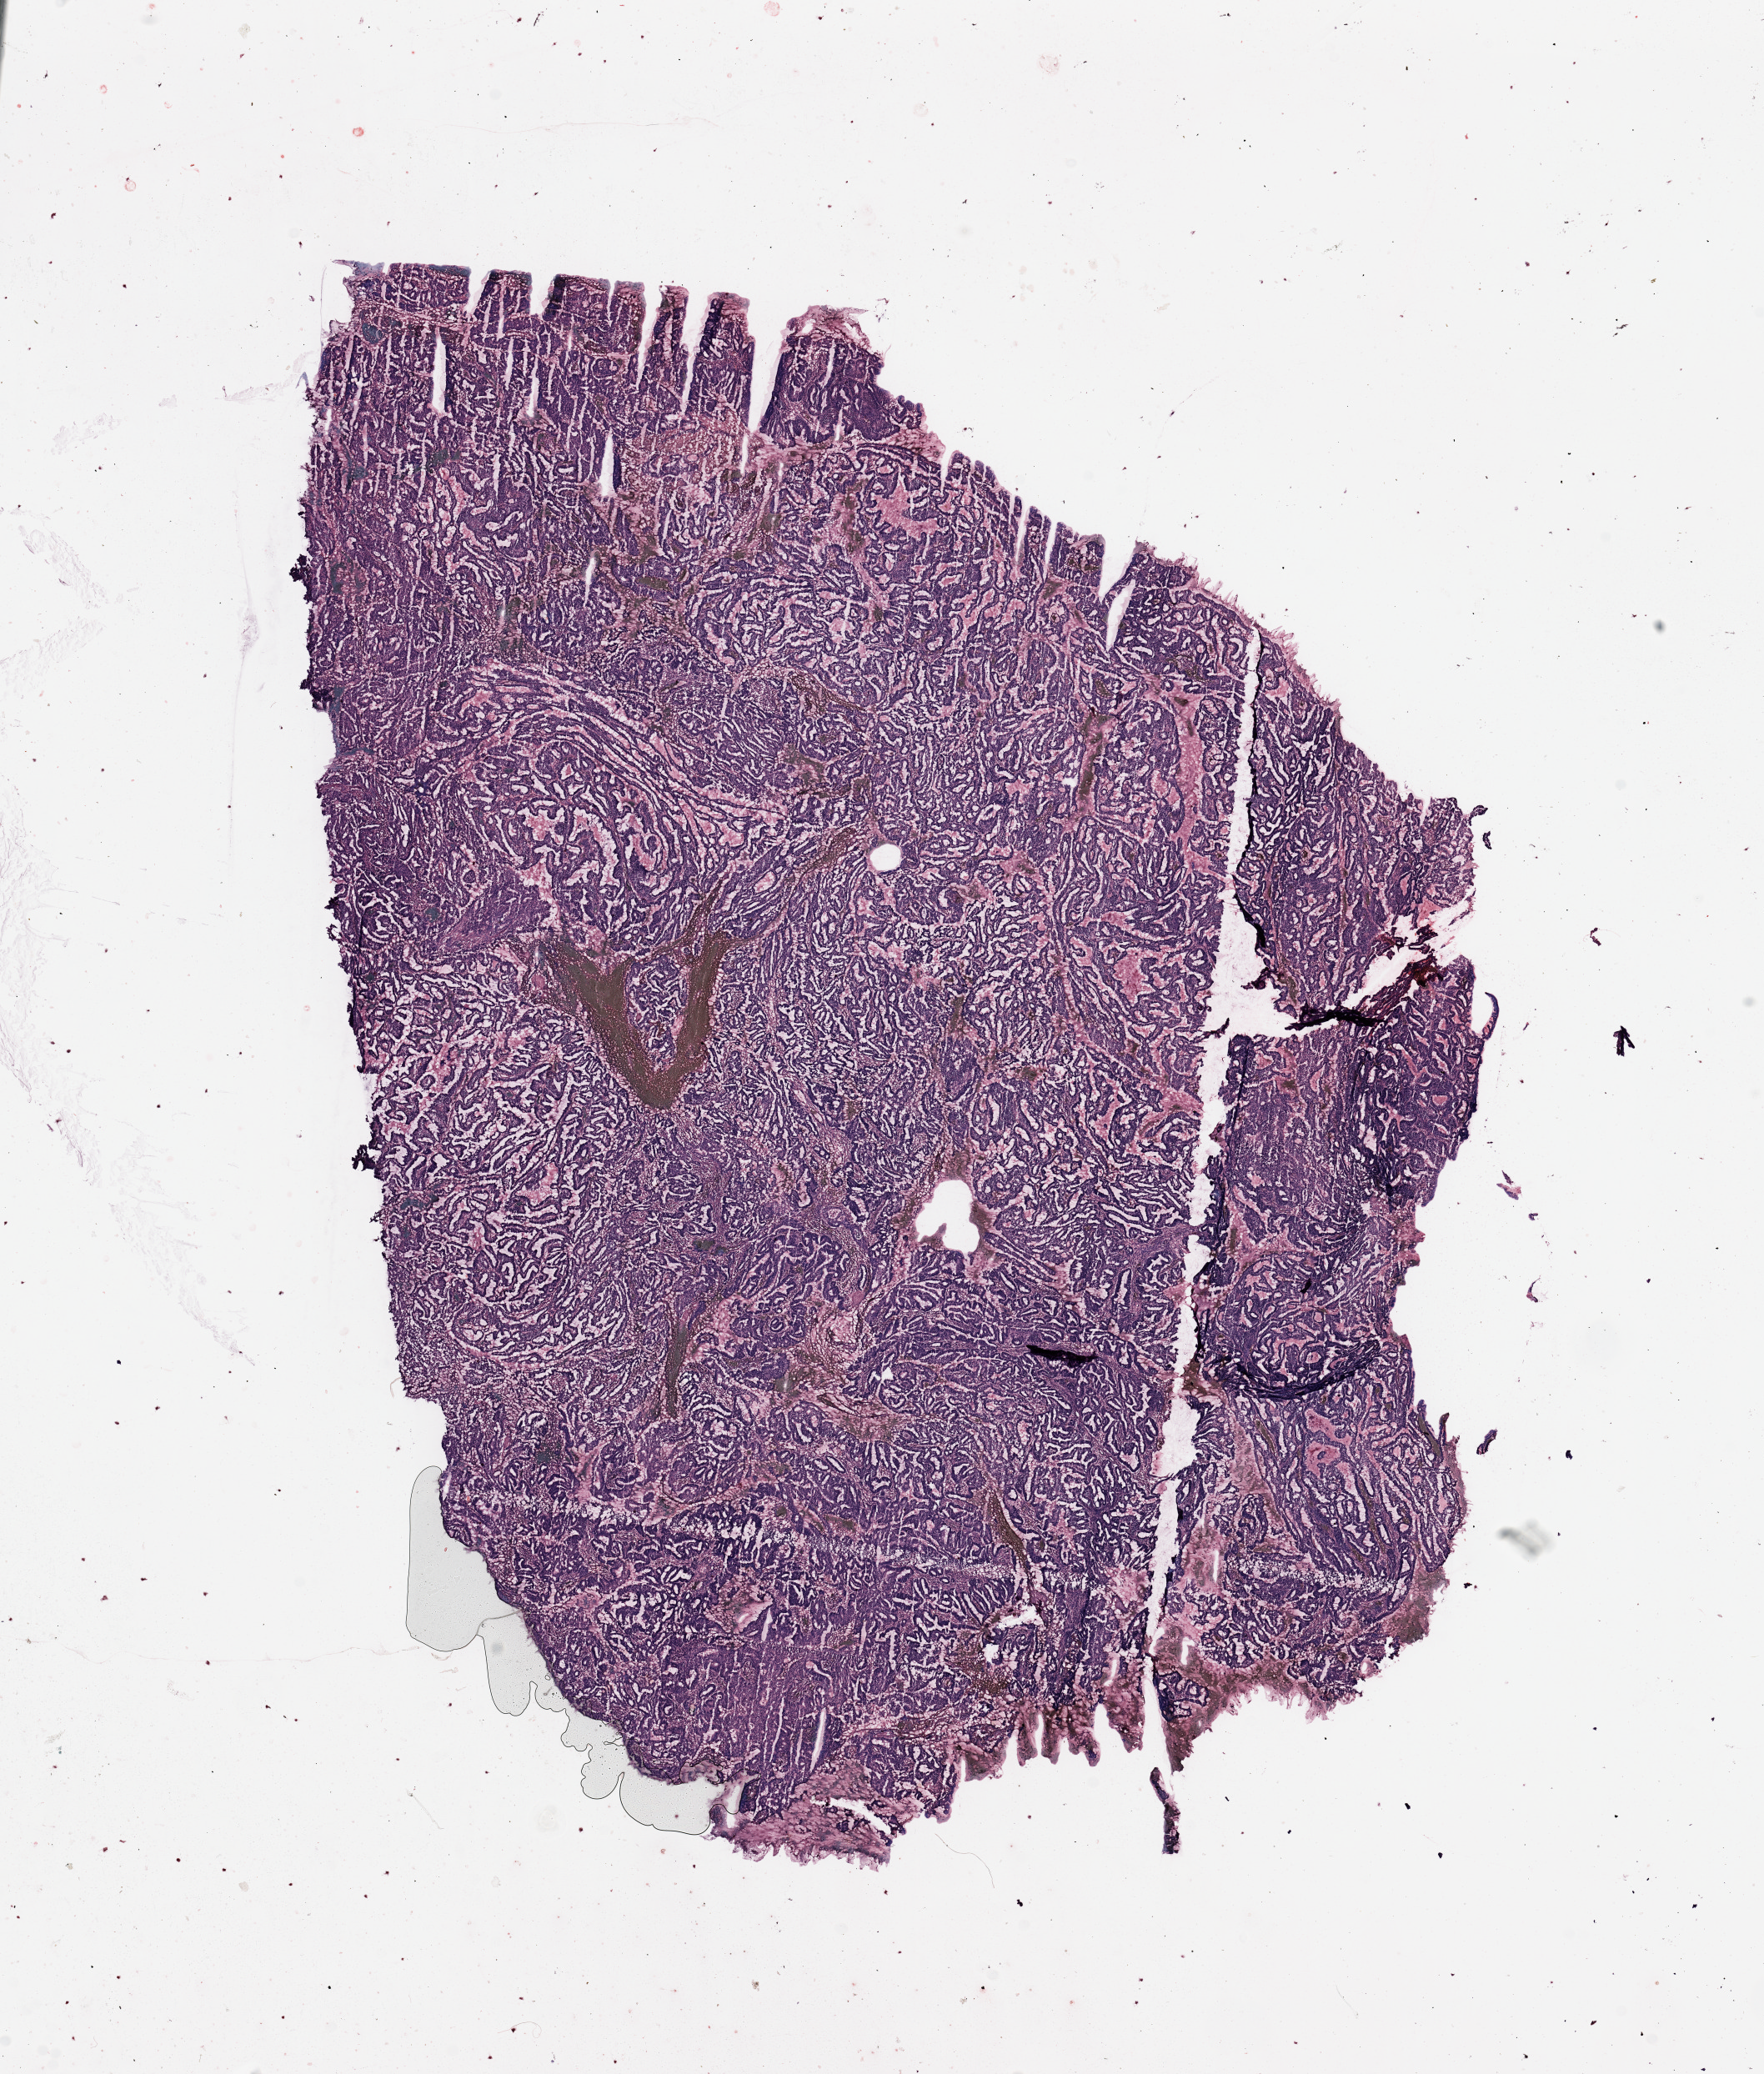
H&E whole-slide image — a low-resolution overview of the entire scanned area, about 16.7 x 19.7 mm (slide scanned at 20x), uterus, tumour tissue. Female, 64 y/o. Histologic grade: G2 (moderately differentiated).
AJCC pathologic stage: I. Diagnosis: Endometrioid adenocarcinoma, NOS.